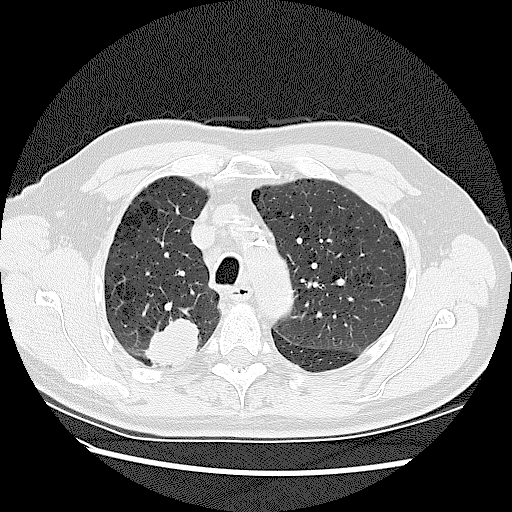
Low-dose screening chest CT, one axial slice; position 95 of 128 along the scan axis; lung window (W 1500 / L -600 HU); 512 × 512 image matrix, field of view 360 × 360 mm.
Annotated regions visible in this slice (expert manual segmentation):
- lesion 2 (tumor, upper lobe of right lung): bounding box [x1, y1, x2, y2] px = [144, 318, 199, 365]